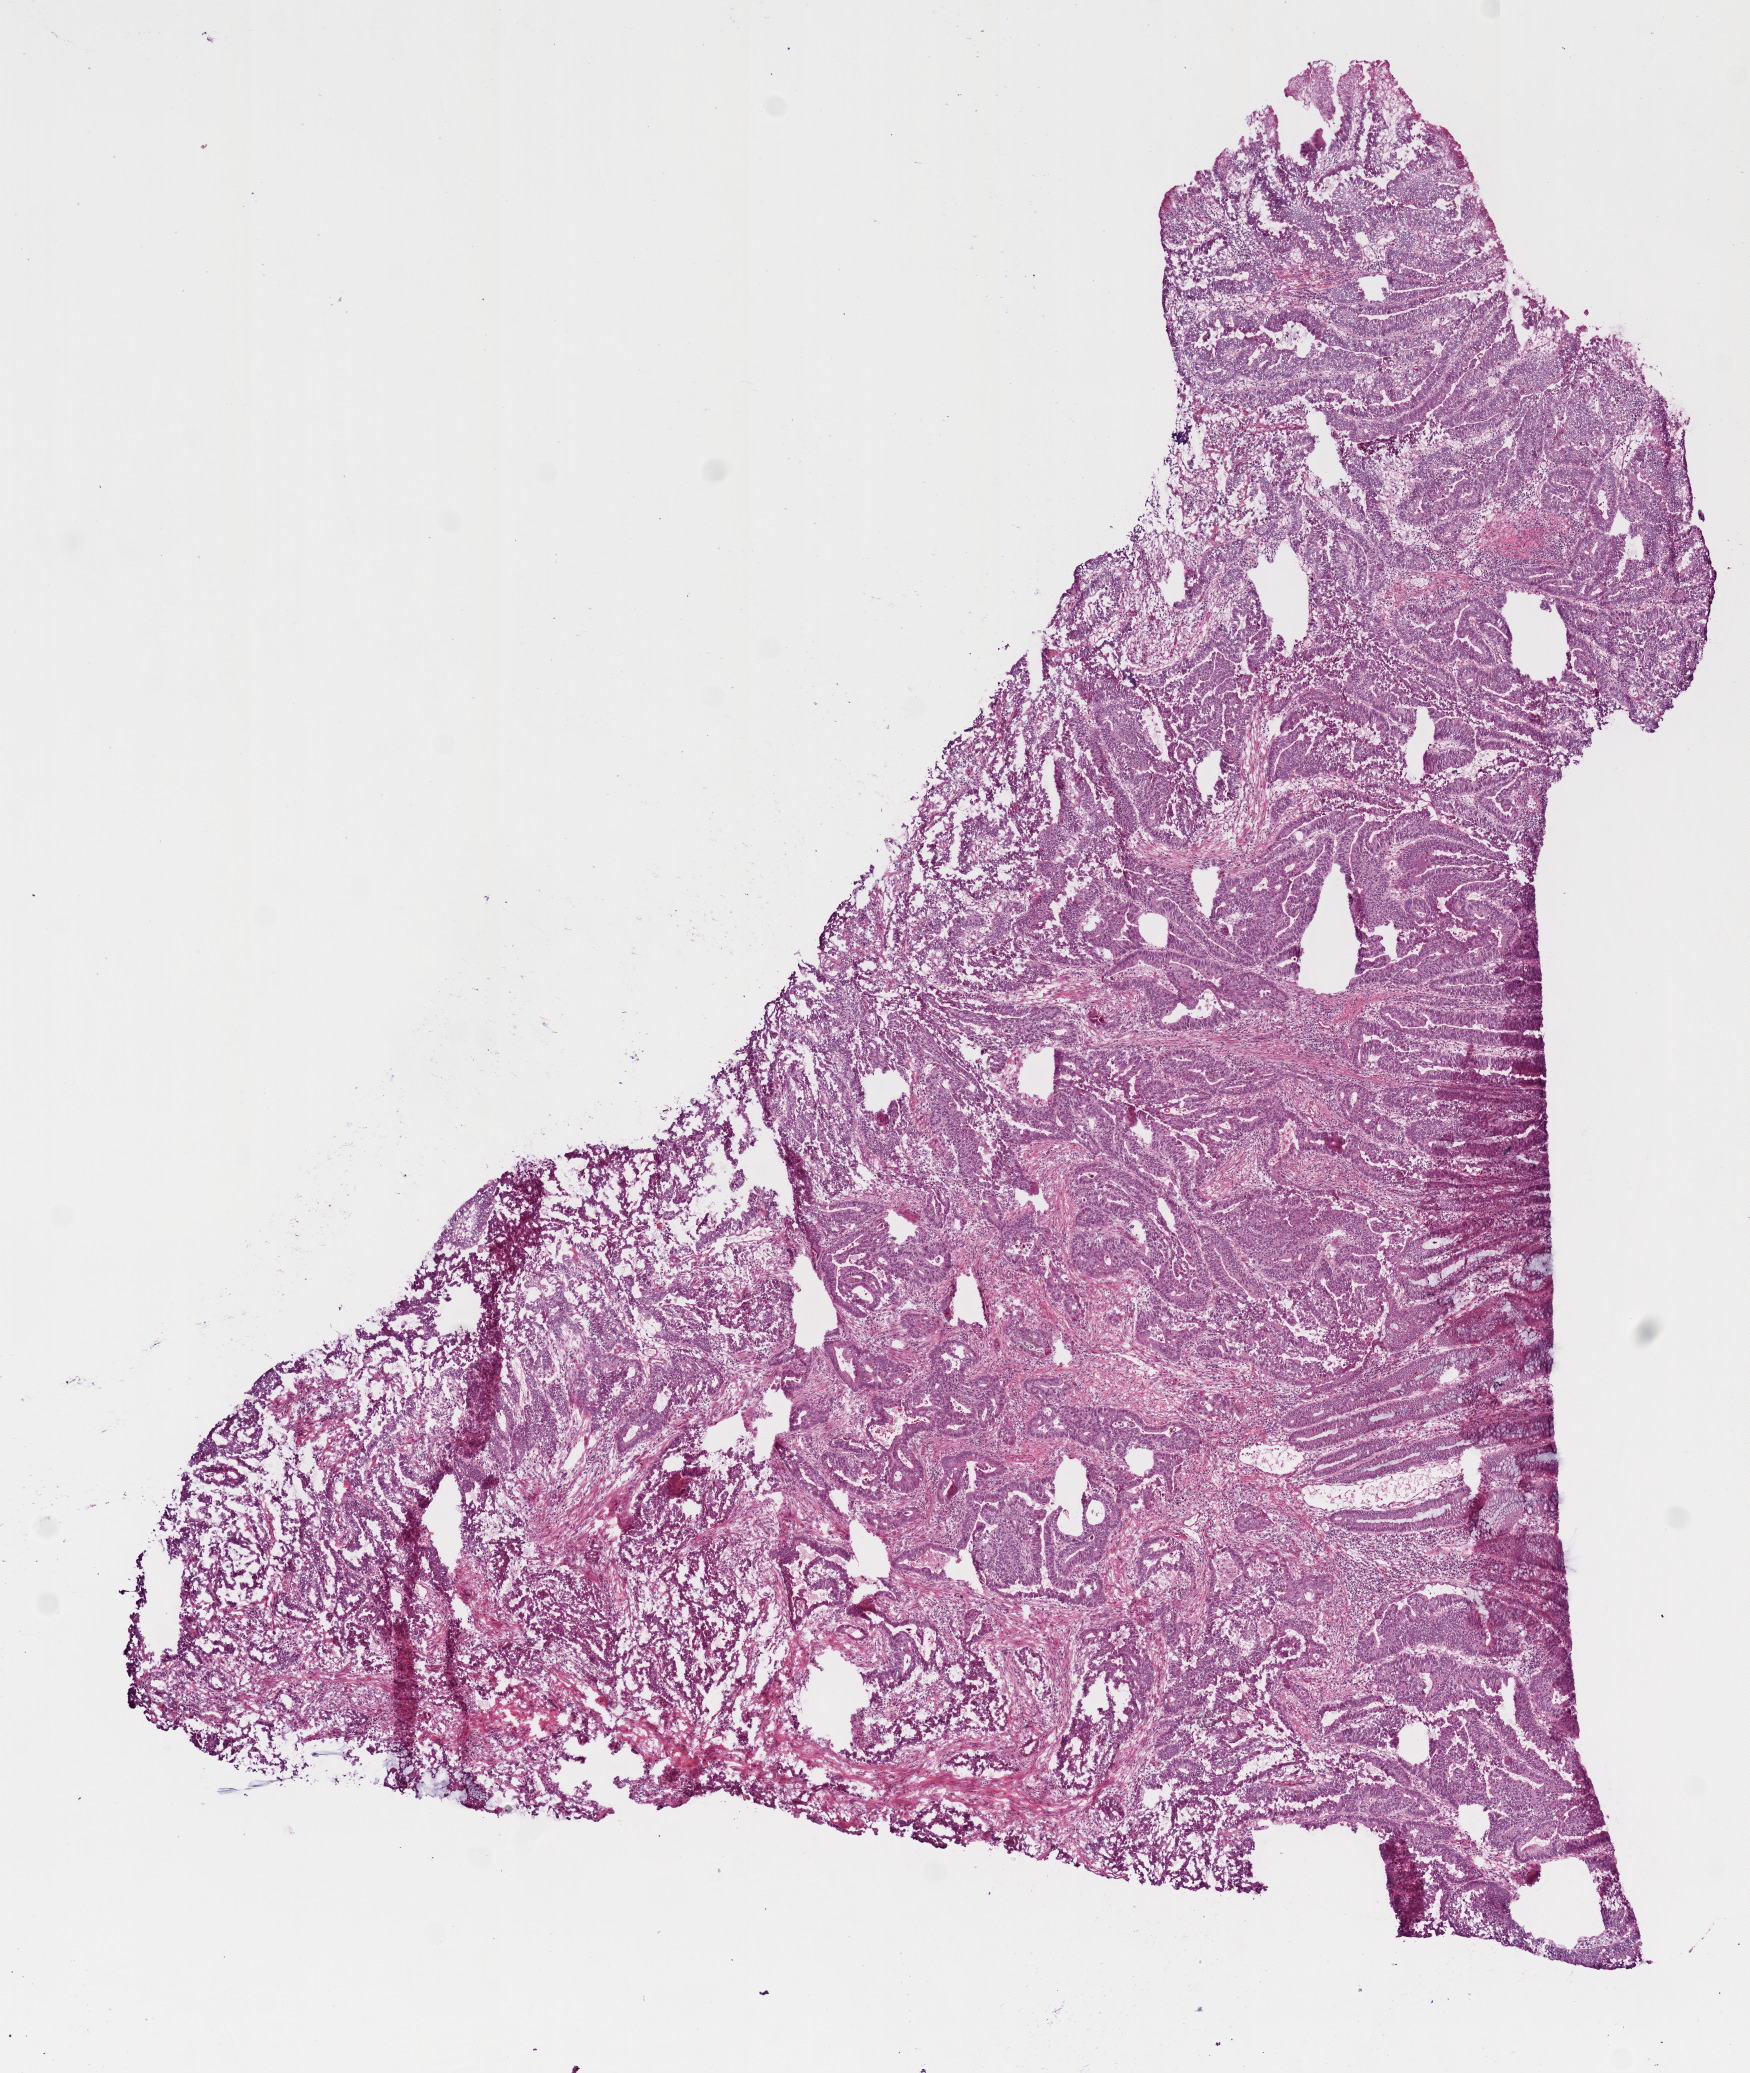
Whole-slide histology image, H&E — whole scanned area (about 7.0 x 8.3 mm) shown as a low-resolution overview; frozen section; primary tumour sample from the colon. Female patient; age at initial diagnosis 74 years. Slide review estimates, as recorded: tumour cells 77%, tumour nuclei 80%, normal cells 3%, stromal cells 10%, necrosis 10%.
* lymph nodes positive (case pathology): 0 of 16 examined
* histologic diagnosis: Adenocarcinoma, NOS (sigmoid colon)
* AJCC pathologic stage: IIA (6th edition)